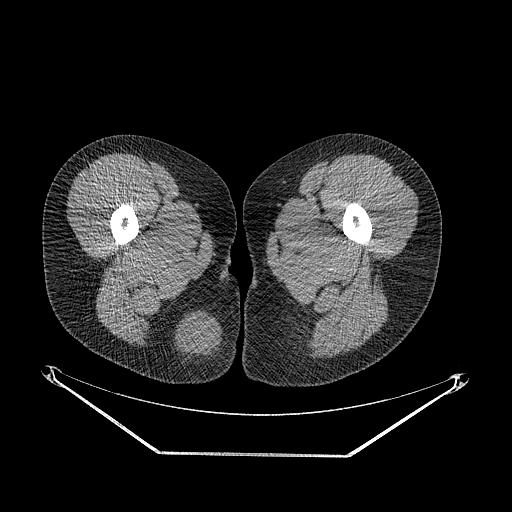
CT of an extremity soft-tissue mass (from a PET/CT study), one axial slice; position 20 of 267 along the scan axis; soft-tissue window (W 400 / L 40 HU); 3.75 mm slice thickness; 512 × 512 image matrix, field of view 500 × 500 mm. Female patient. Case-level facts recorded for this patient, not image findings: histological type: epithelioid sarcoma; grade: intermediate; site of the primary tumour: right buttock.
Annotated regions visible in this slice (expert contour drawn on MRI and transferred to this co-registered scan by the dataset authors):
- gross tumour volume including surrounding oedema: bounding box <174,308,232,380> (left, top, right, bottom; pixels)
- gross tumour volume (mass): <178,315,220,355>